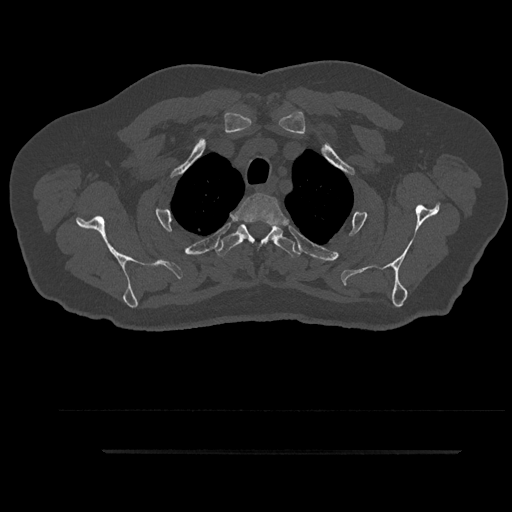
CT including the spine, one axial slice; slice 736 of 797 in the series (ordered by position); reconstruction kernel Br40s/3; 120 kVp; bone window (W 1800 / L 400 HU); 0.5 mm slice thickness; 512 × 512 image matrix. Male patient, age 63 years. Case-level facts recorded for this patient, not image findings: primary cancer: renal.
Annotated regions visible in this slice (semi-automatically segmented with operator editing):
- T2 vertebra: bounding box [x1, y1, x2, y2] px = [235, 193, 285, 242]
- T3 vertebra: [215, 223, 302, 258]